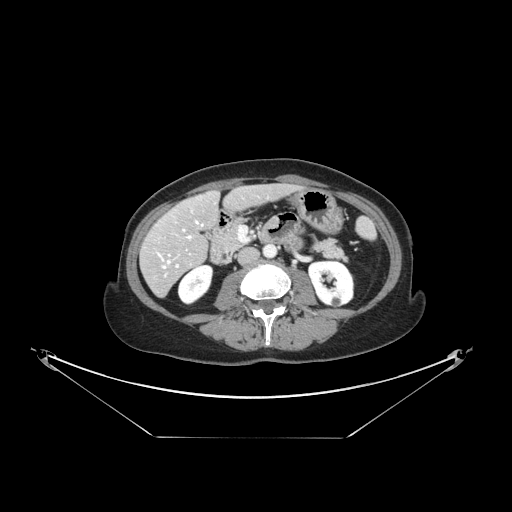
Contrast-enhanced abdominal CT, one axial slice. Position 51 of 148 along the scan axis. Intravenous contrast given. Soft-tissue window (W 400 / L 40 HU). 512 × 512 image matrix. Female patient, age 73 years. From the clinical record (not read from this slice): diagnosis: colorectal cancer liver metastases, imaged before liver resection; multiple liver metastases: no; largest metastasis: 1 cm; disease in both lobes: no.
Annotated regions visible in this slice (manually delineated by an expert):
- hepatic veins: bounding box <158,222,198,268> (left, top, right, bottom; pixels)
- liver: <143,184,293,295>
- planned liver remnant (the part of the liver to remain after resection): <162,185,292,247>